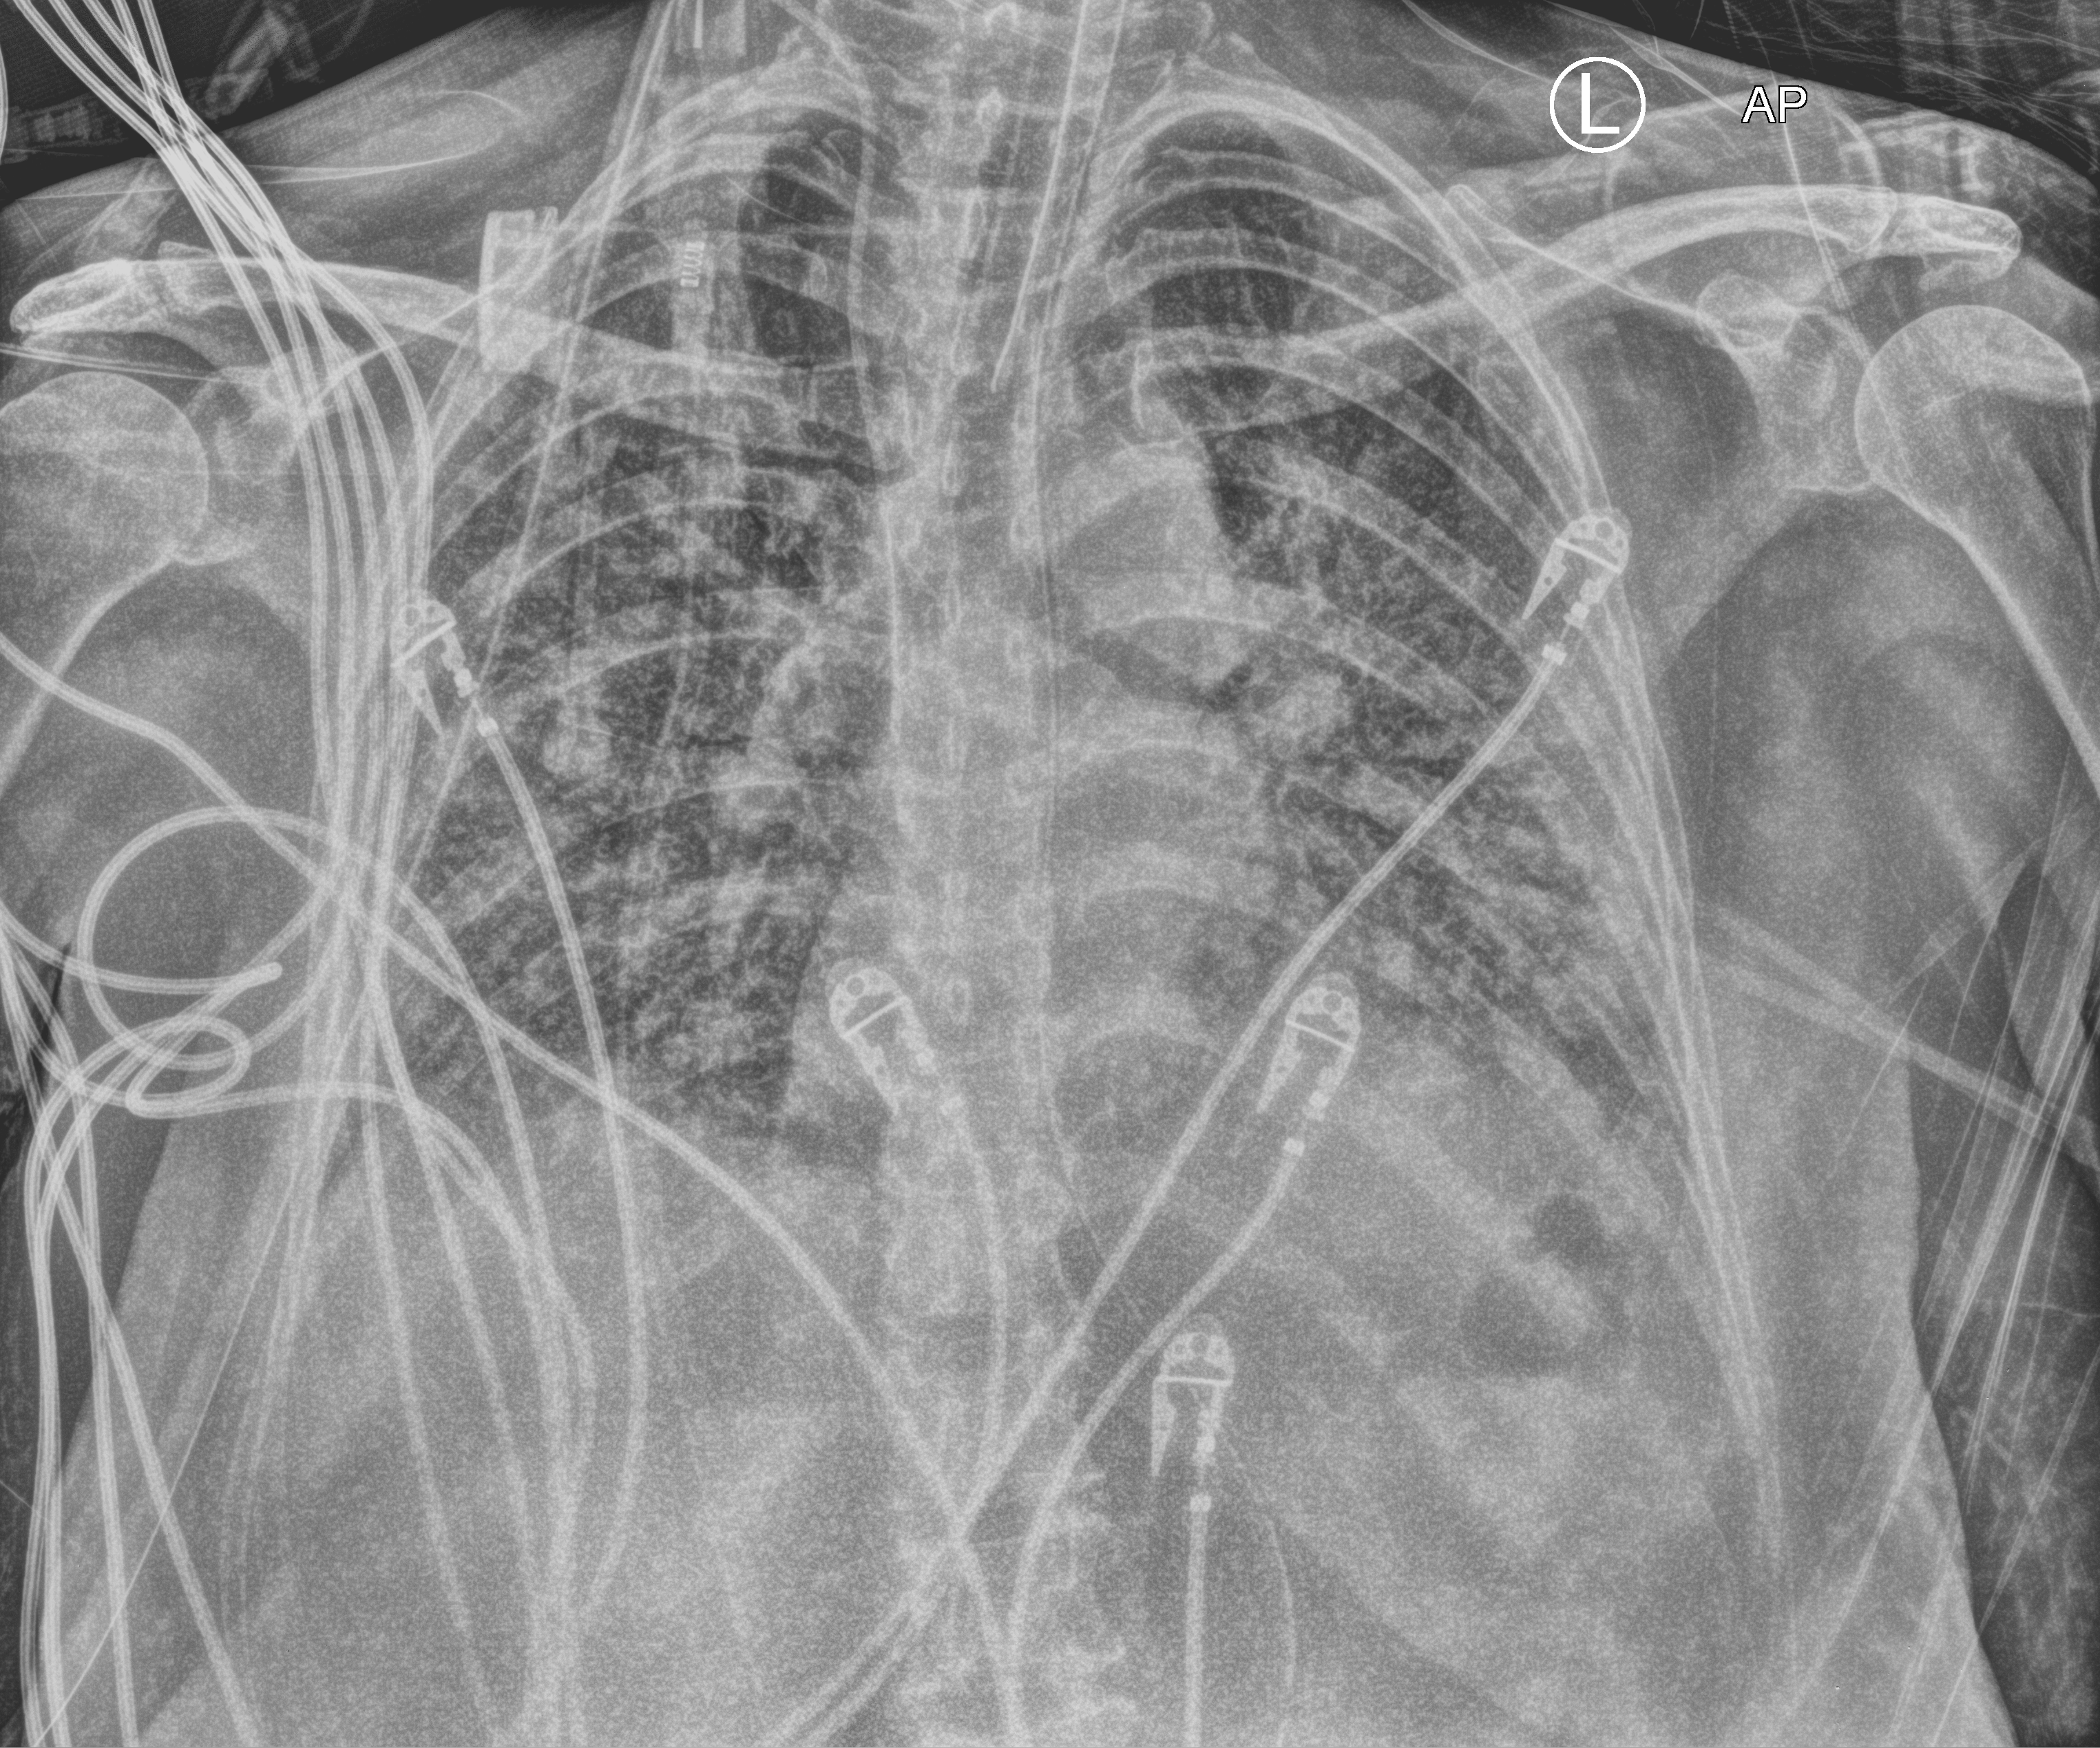
Chest X-ray (portable); anteroposterior (AP) projection. Female patient hospitalised with COVID-19, age 60–74 years.
Hospital-stay facts (about this admission, not read from this image; timing relative to this image not recorded): admitted to intensive care during this hospital stay: yes.